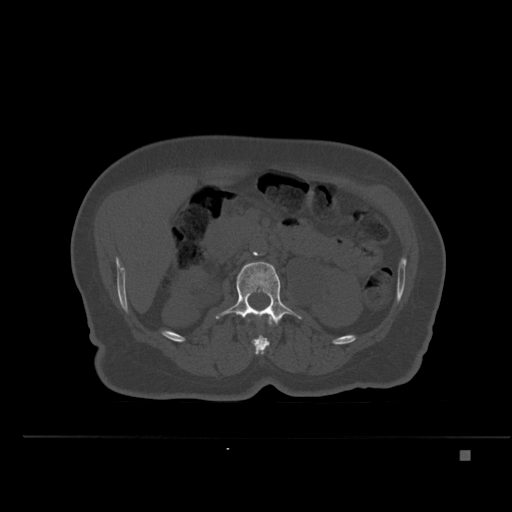
CT including the spine, one axial slice. Slice 219 of 477 in the series (ordered by position). Bone window (W 1800 / L 400 HU). 1.5 mm slice thickness. 512 × 512 image matrix, field of view 422 × 422 mm. Female patient, age 74 years. From the clinical record (not read from this slice): primary cancer: colon.
Structures marked on this image (semi-automatic segmentation, software-assisted and operator-edited):
- L1 vertebra: box from (x=247, y=313) to (x=276, y=354) px
- L2 vertebra: (x=216, y=261)–(x=301, y=325)